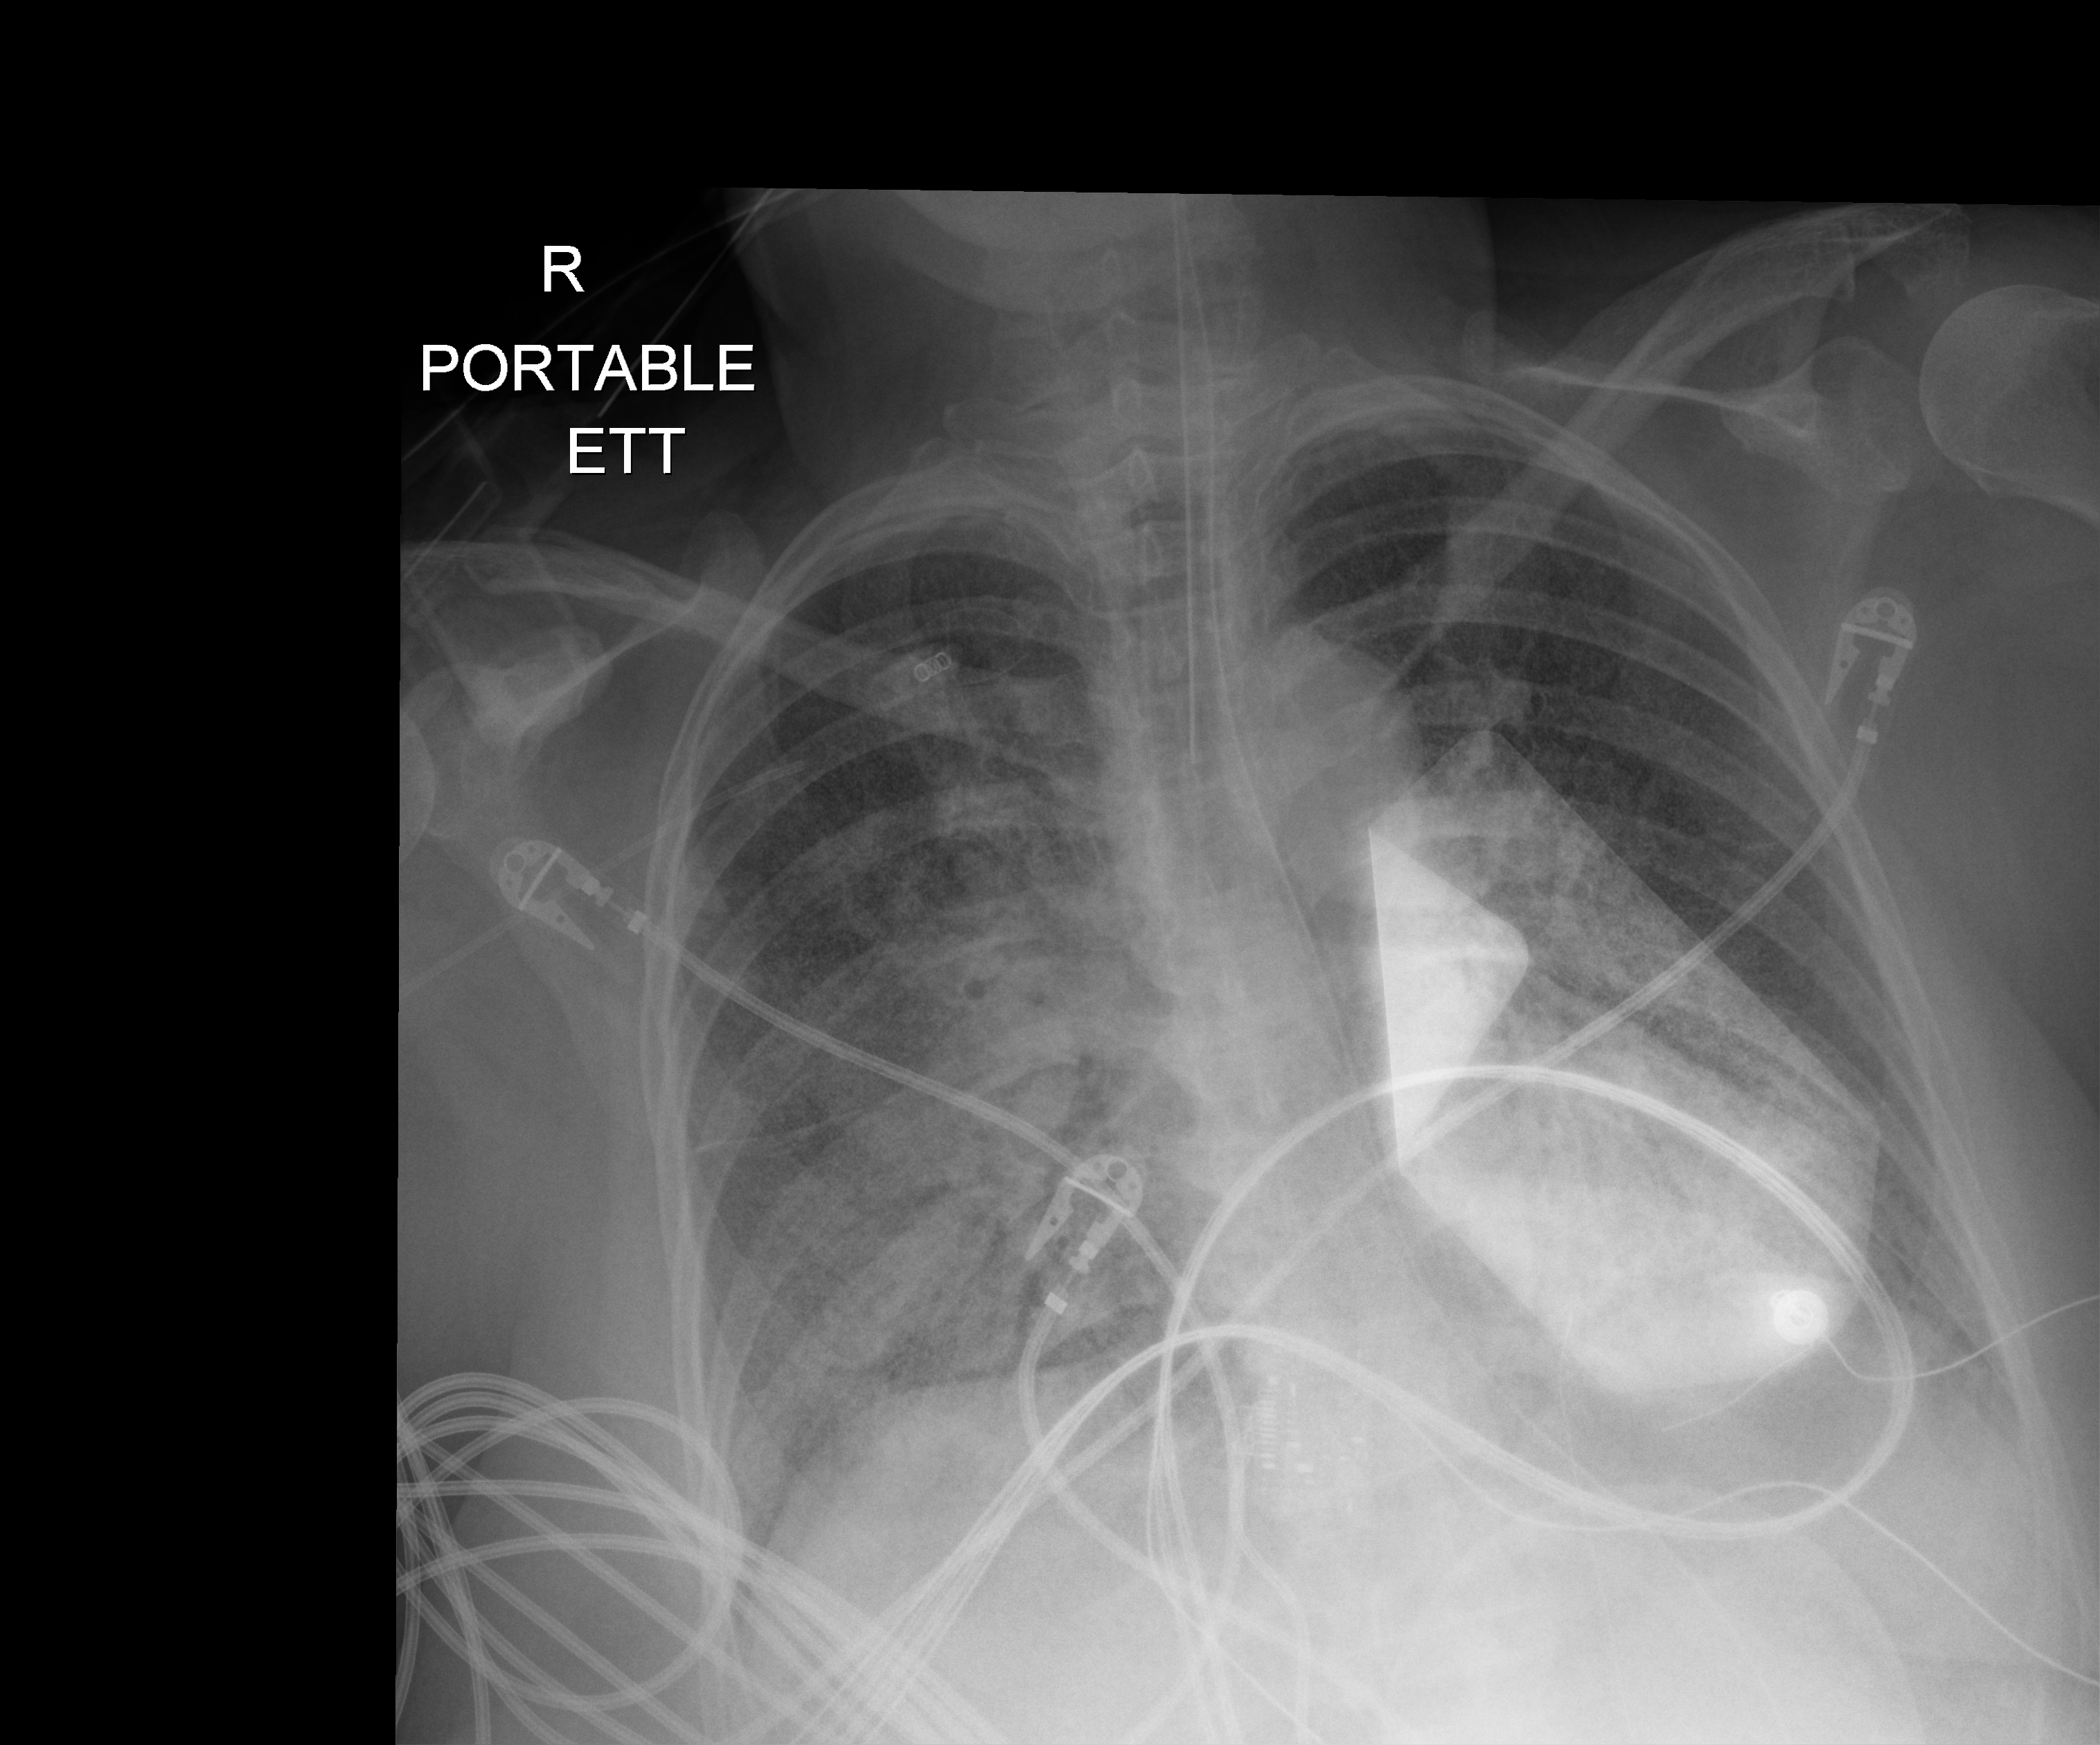
Bedside chest radiograph (digital radiography); anteroposterior (AP) projection. Patient hospitalised with COVID-19; female, aged 60–74 years.
From the hospital-stay record, not from the radiograph (when in the stay this image was taken is not recorded): diabetes (admission record): no.